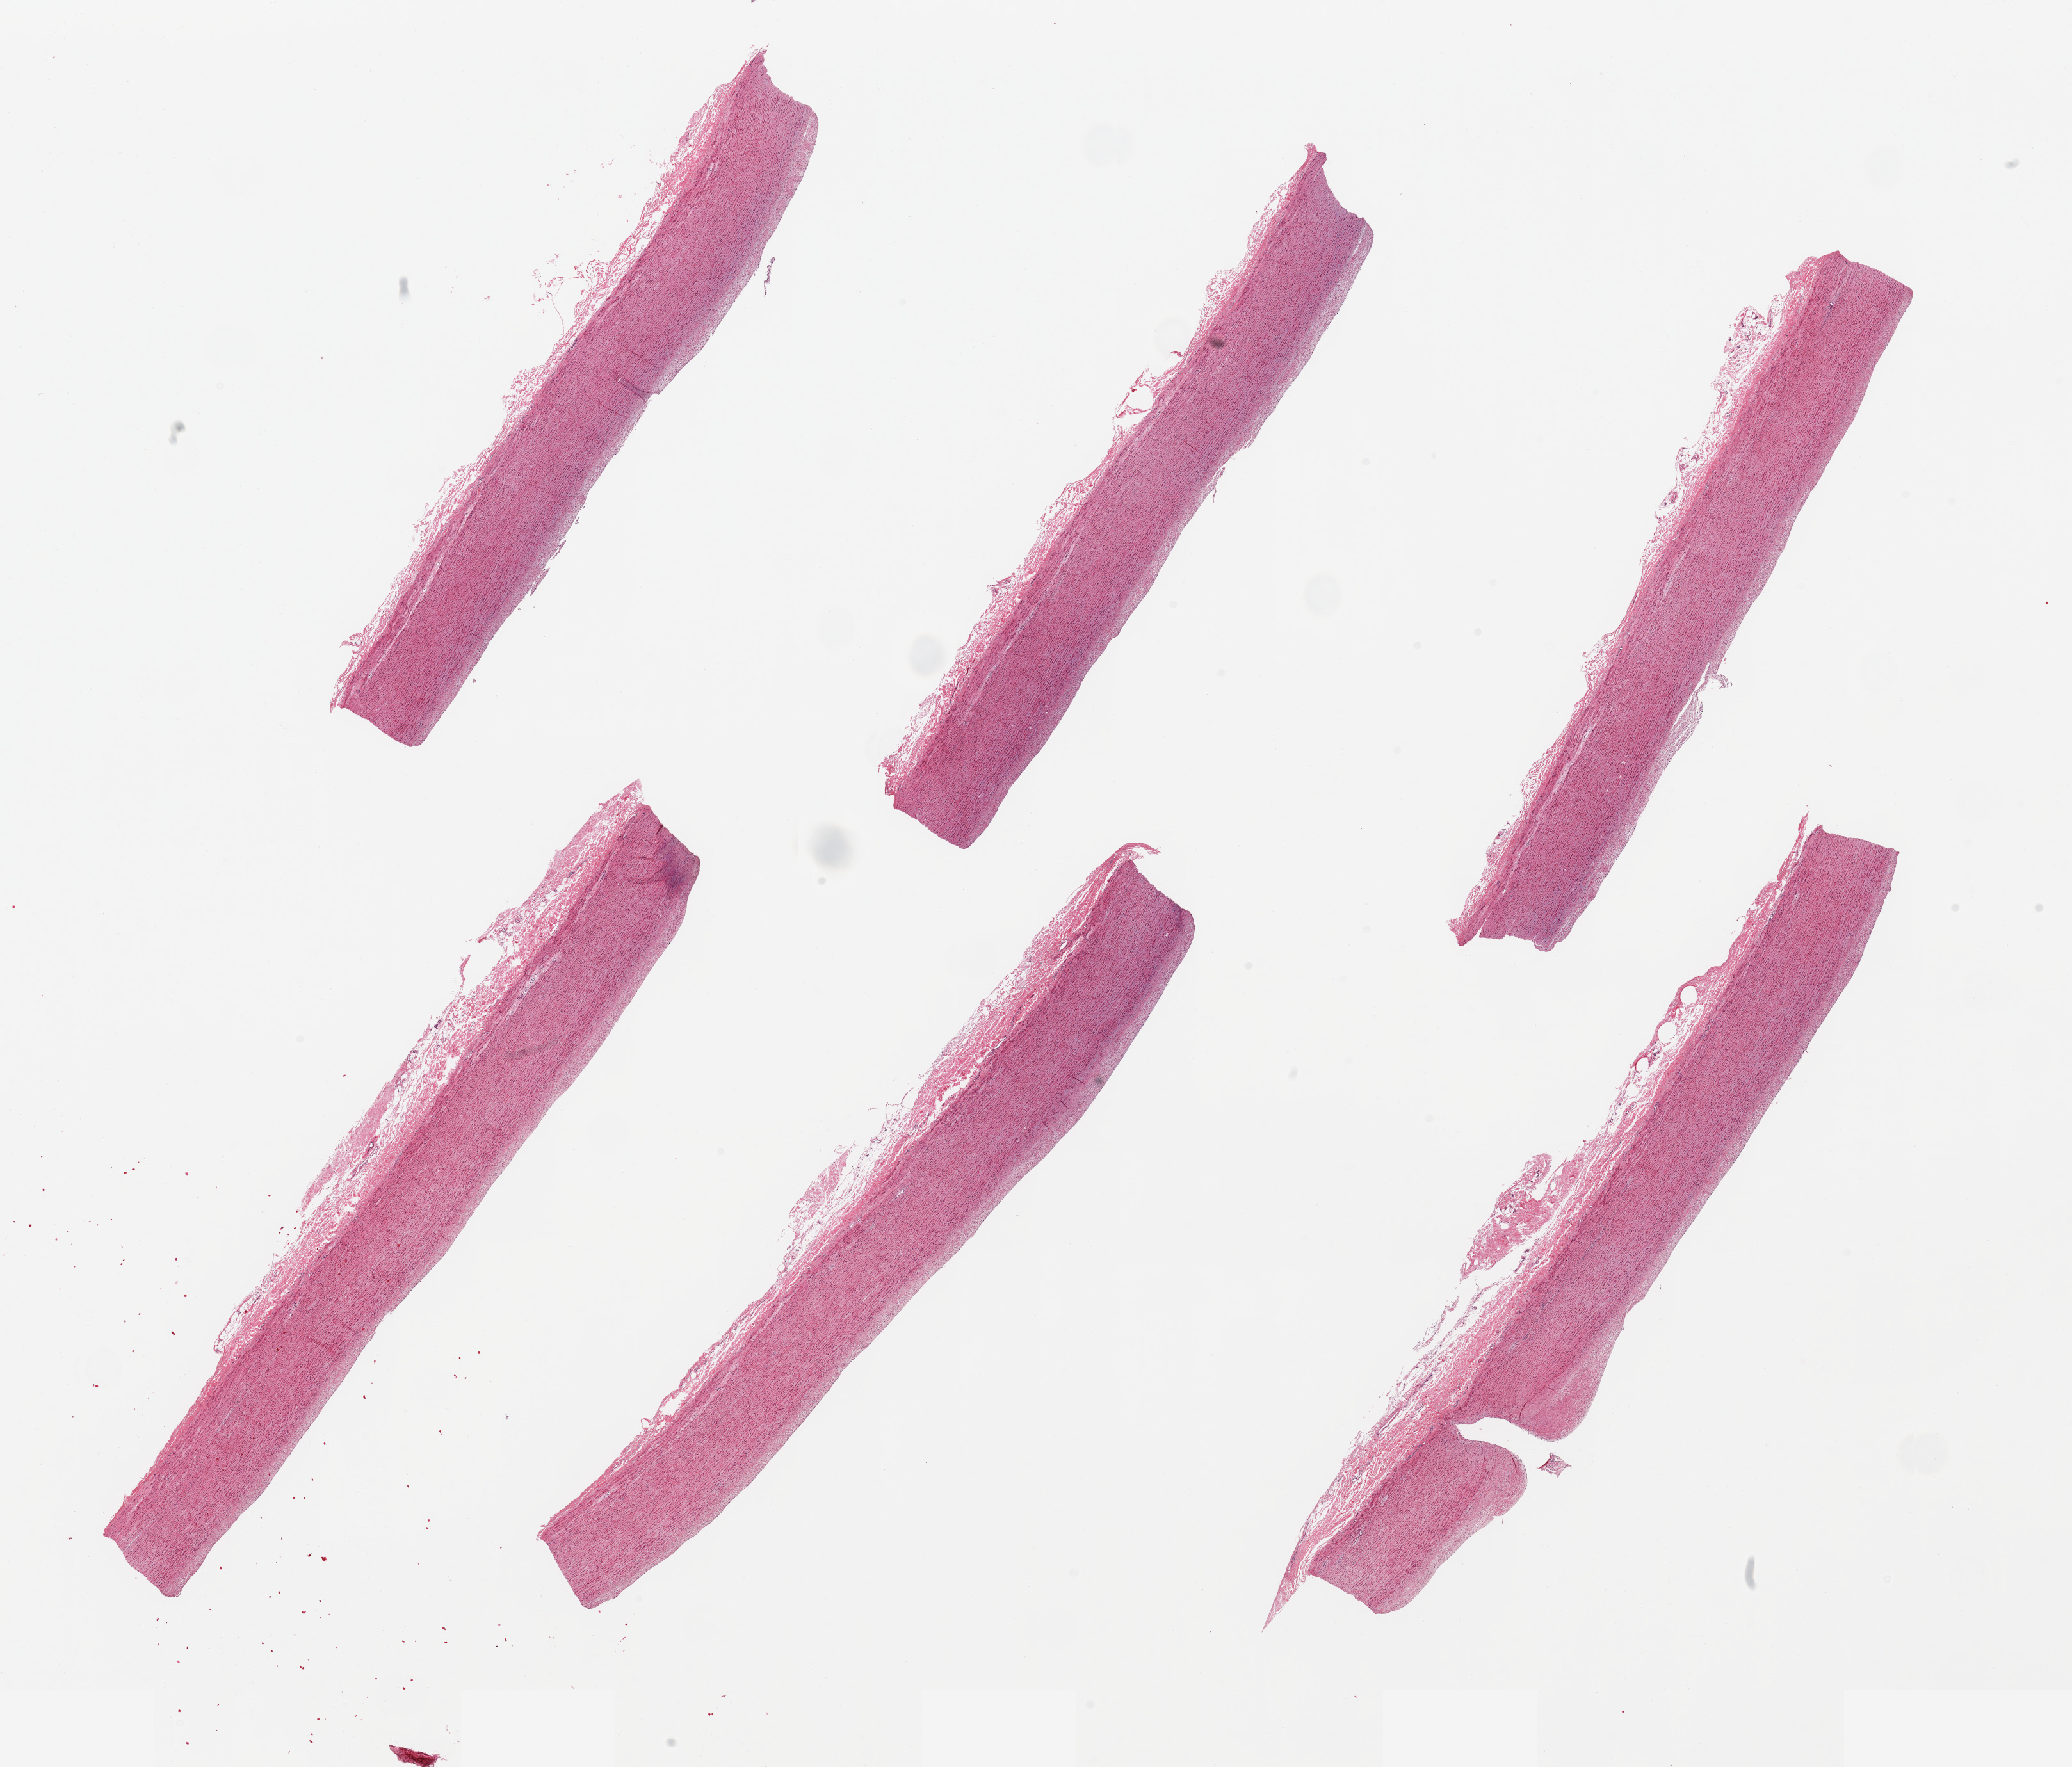
Whole-slide image, hematoxylin and eosin (H&E) stain, a low-resolution overview of the entire scanned area, about 25.6 x 21.8 mm (slide scanned at 20x). PAXgene-fixed, paraffin-embedded tissue. Target tissue: aorta. Tissue donor sample. Male donor.
• review note (as recorded): 6 pieces; no lesions; well trimmed